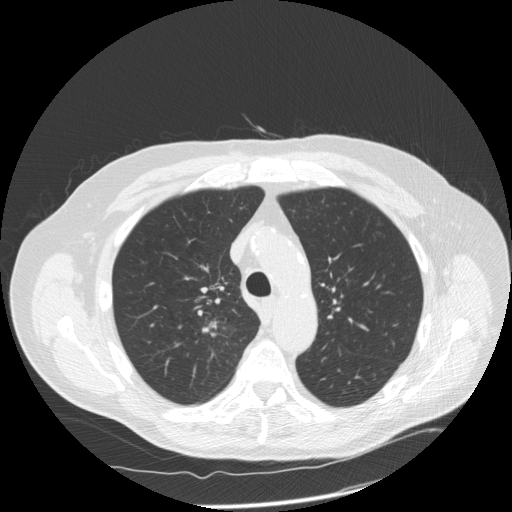
Axial slice from a low-dose chest CT screening exam; third screening round (two years after baseline); lung window (W 1500 / L -600 HU); 2.5 mm slice thickness; slice 47 of 166 in the series. Male, age 69 years at enrolment.
- Expert-annotated lung lesion, bounding box <181,306,243,355> (left, top, right, bottom; pixels).
- The exam's reader record, not a measurement of the box and not confirmed to be the same lesion: non-calcified nodule or mass ≥4 mm, right upper lobe, 18 × 17 mm, spiculated (stellate) margins, soft tissue attenuation, pre-existing on the prior screen: no.
- Participant outcome: lung cancer diagnosed 13 days after this screen — squamous cell carcinoma, NOS, right upper lobe, poorly differentiated (G3), stage IA (AJCC 6th edition), 22 mm at pathology.